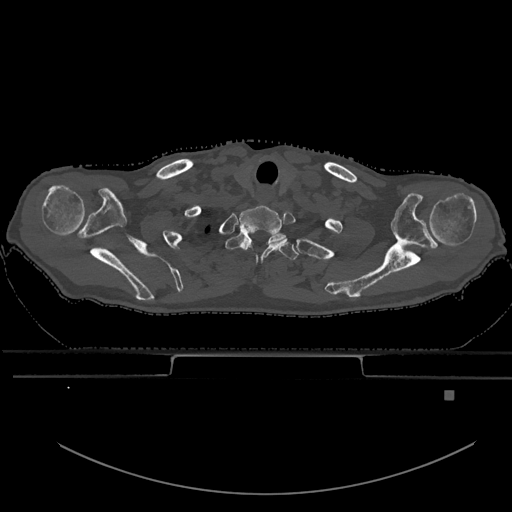
CT including the spine, one axial slice; position 552 of 969 along the scan axis; bone window (W 1800 / L 400 HU); 0.5 mm slice thickness; 512 × 512 image matrix, field of view 456 × 456 mm. Patient: male, 82 years. Case-level facts recorded for this patient, not image findings: primary cancer: prostate.
Annotated regions visible in this slice (semi-automatically segmented with operator editing):
- T1 vertebra: box from (x=226, y=231) to (x=299, y=260) px